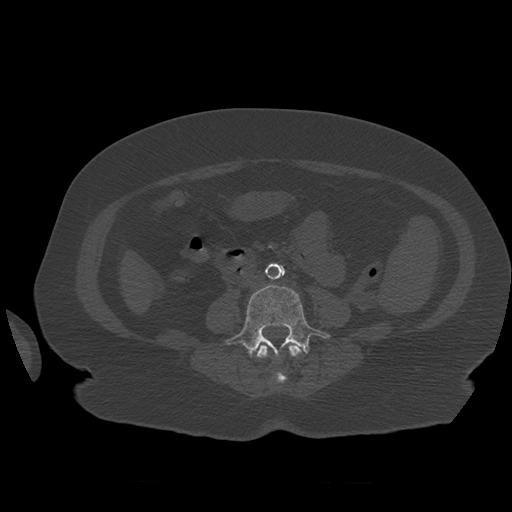
CT including the spine, one axial slice; position 211 of 399 along the scan axis; 120 kVp; bone window (W 1800 / L 400 HU); 512 × 512 image matrix, field of view 404 × 404 mm. Patient age 81 years. From the clinical record (not read from this slice): primary cancer: renal.
Annotated regions visible in this slice (semi-automatic segmentation, software-assisted and operator-edited):
- L3 vertebra: box from (x=256, y=344) to (x=304, y=383) px
- L4 vertebra: (x=226, y=285)–(x=331, y=357)